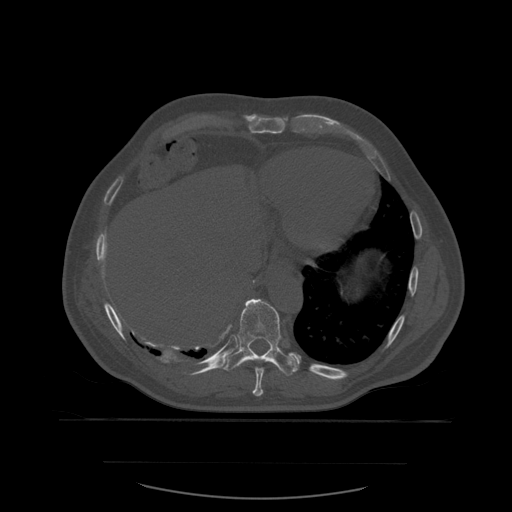
CT including the spine, one axial slice. Position 324 of 590 along the scan axis. Bone window (W 1800 / L 400 HU). 1.25 mm slice thickness. 512 × 512 image matrix, field of view 479 × 479 mm. Patient age 71 years. From the clinical record (not read from this slice): primary cancer: lung.
Structures marked on this image (semi-automatically segmented with operator editing):
- T10 vertebra: bounding box (x1, y1, x2, y2) in pixels: (226, 299, 299, 376)
- T9 vertebra: (253, 367, 265, 397)